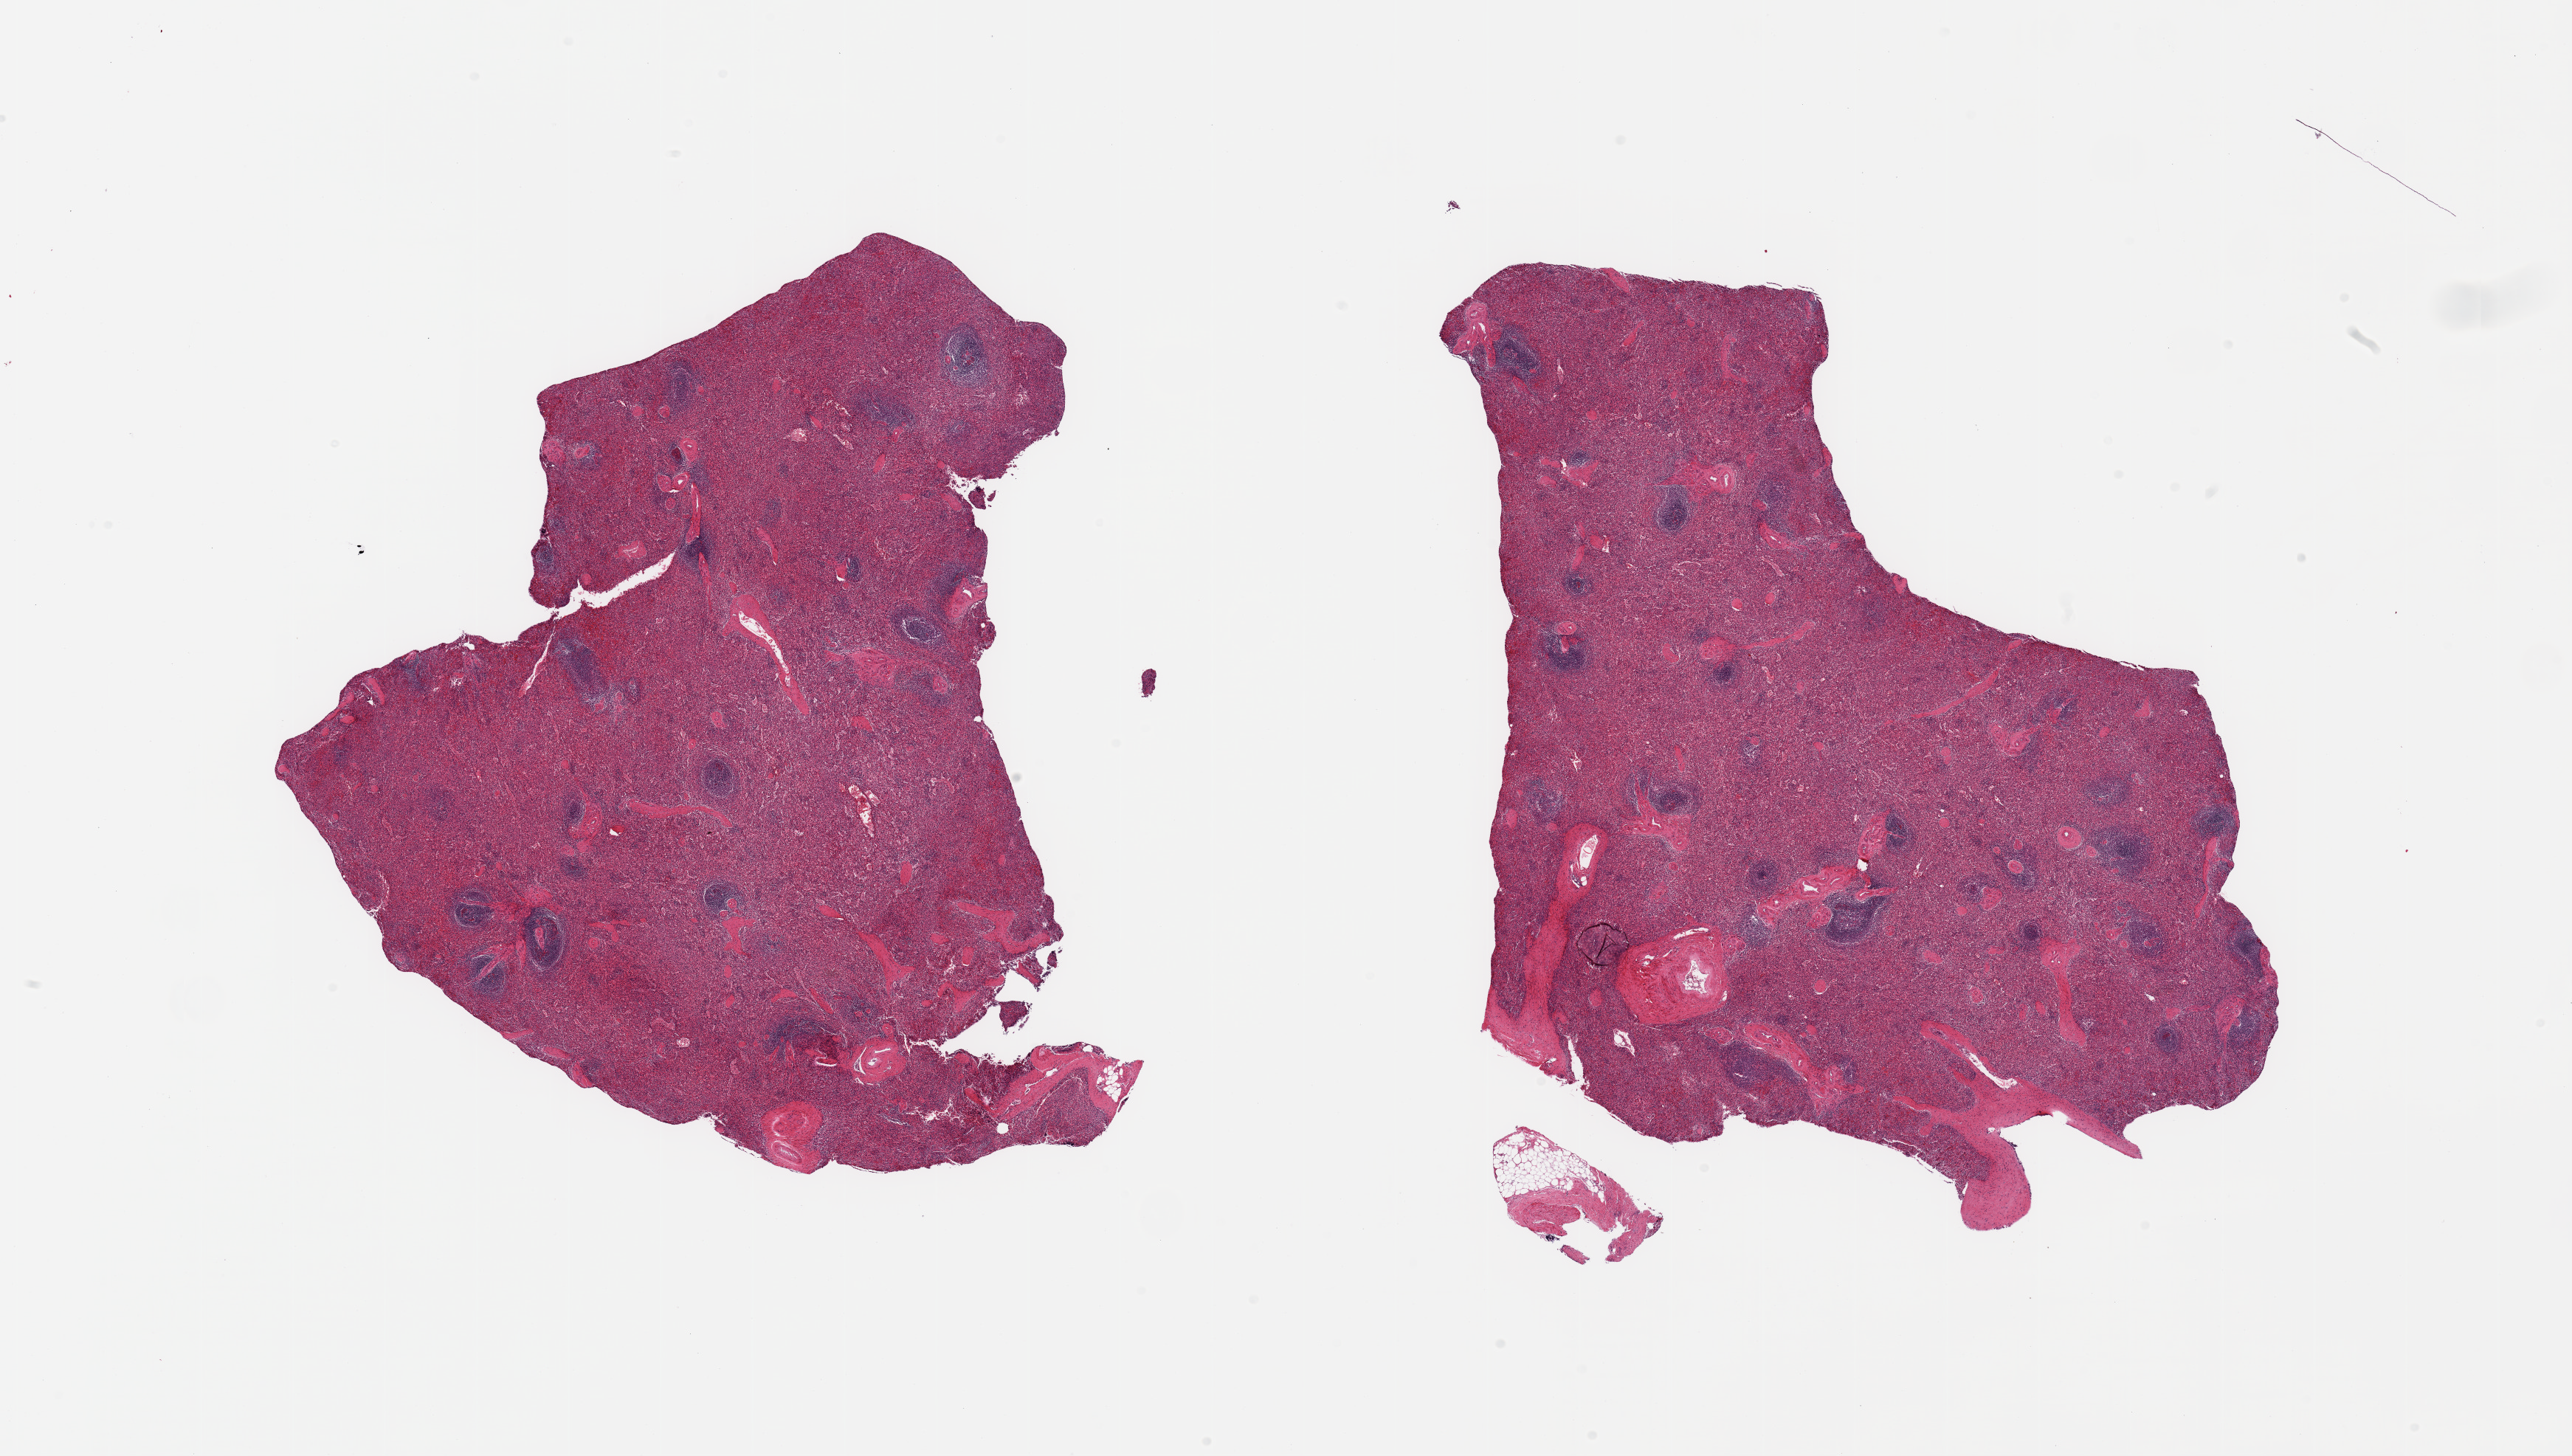
Digitized H&E-stained section, low-resolution overview of the scanned area, about 27.6 x 15.6 mm. PAXgene-fixed, paraffin-embedded tissue. Sampled site (target tissue): spleen. Donor tissue sample.
Reviewer comment on this tissue sample: 2 pieces; congestion.